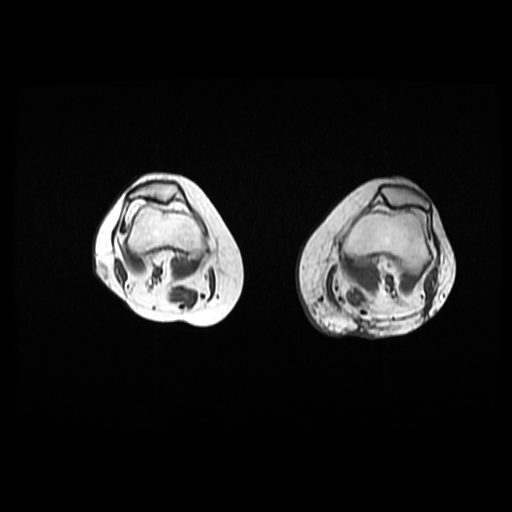
MRI of an extremity soft-tissue mass, one axial slice; position 11 of 42 along the scan axis; 6 mm slice thickness; 512 × 512 image matrix. Female patient. From the clinical record (not read from this slice): histological type: pleomorphic leiomyosarcoma; grade: high; site of the primary tumour: left thigh.
Annotated regions visible in this slice (manually delineated by an expert):
- gross tumour volume including surrounding oedema: bounding box <323,264,342,301> (left, top, right, bottom; pixels)